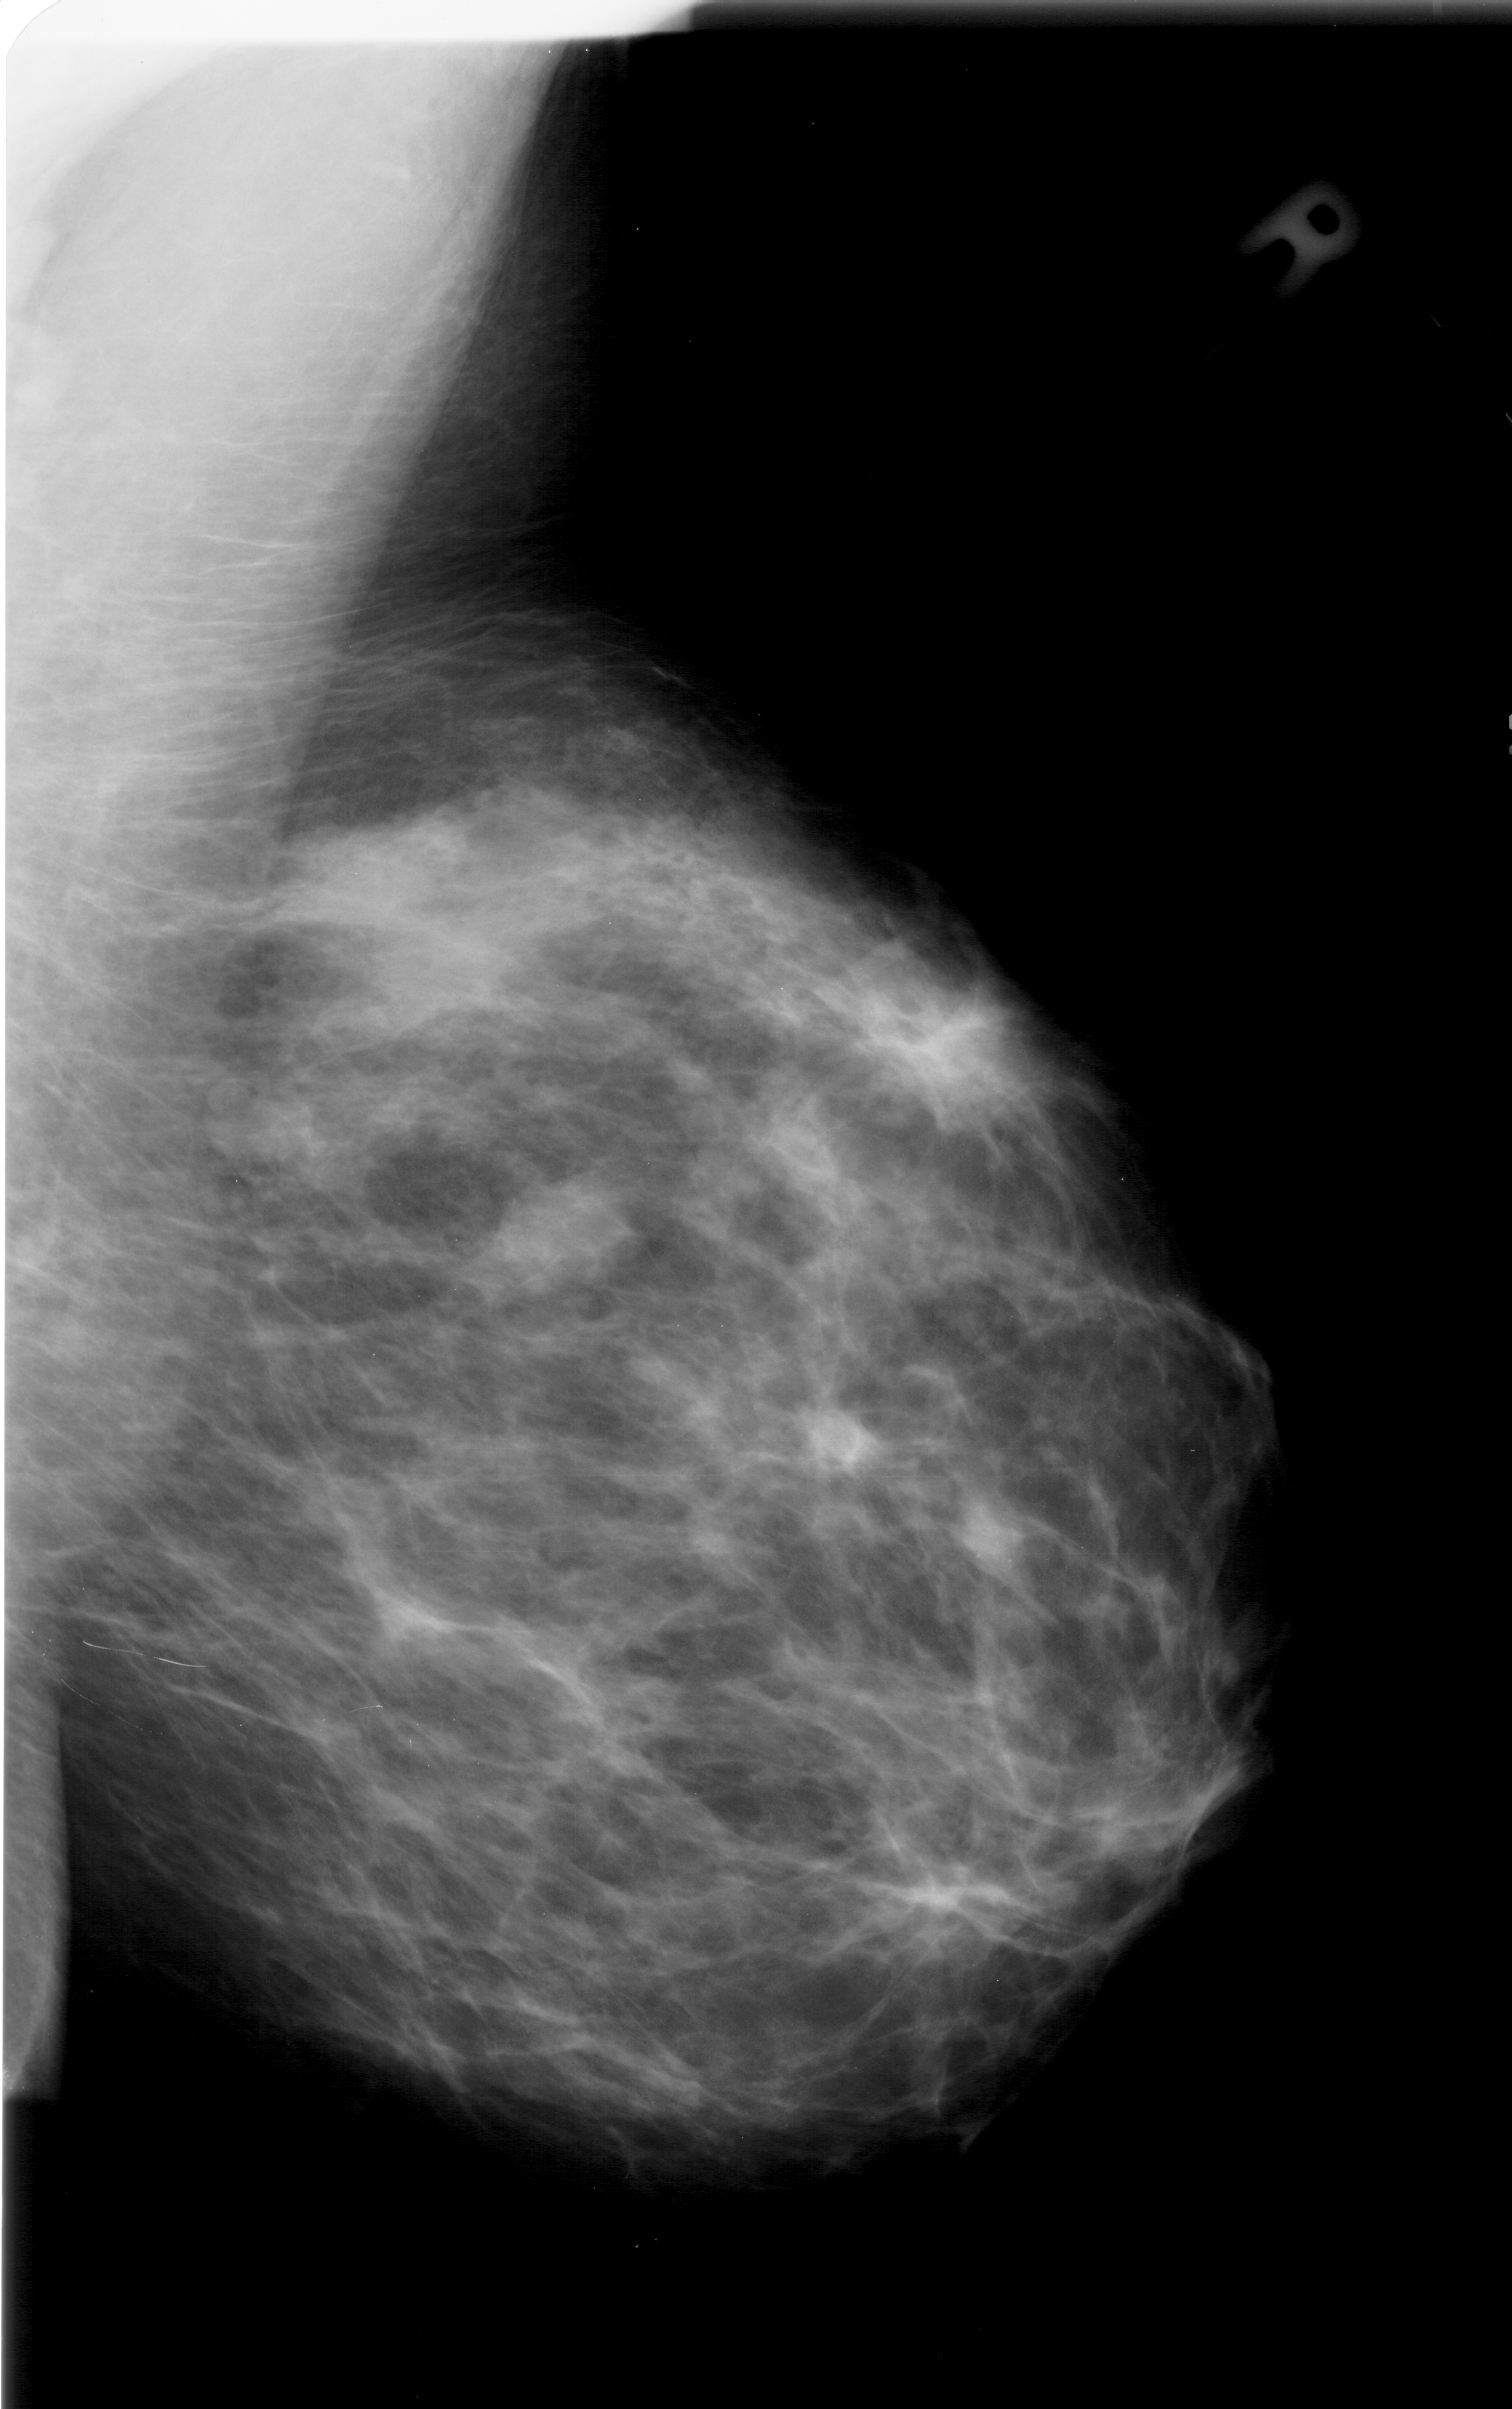
Digitized screen-film mammogram, right breast, MLO view, breast composition: almost entirely fatty (BI-RADS density category 1 of 4).
- Mass, shape lobulated, margins ill defined; BI-RADS assessment category 4; pathology (as recorded): benign.